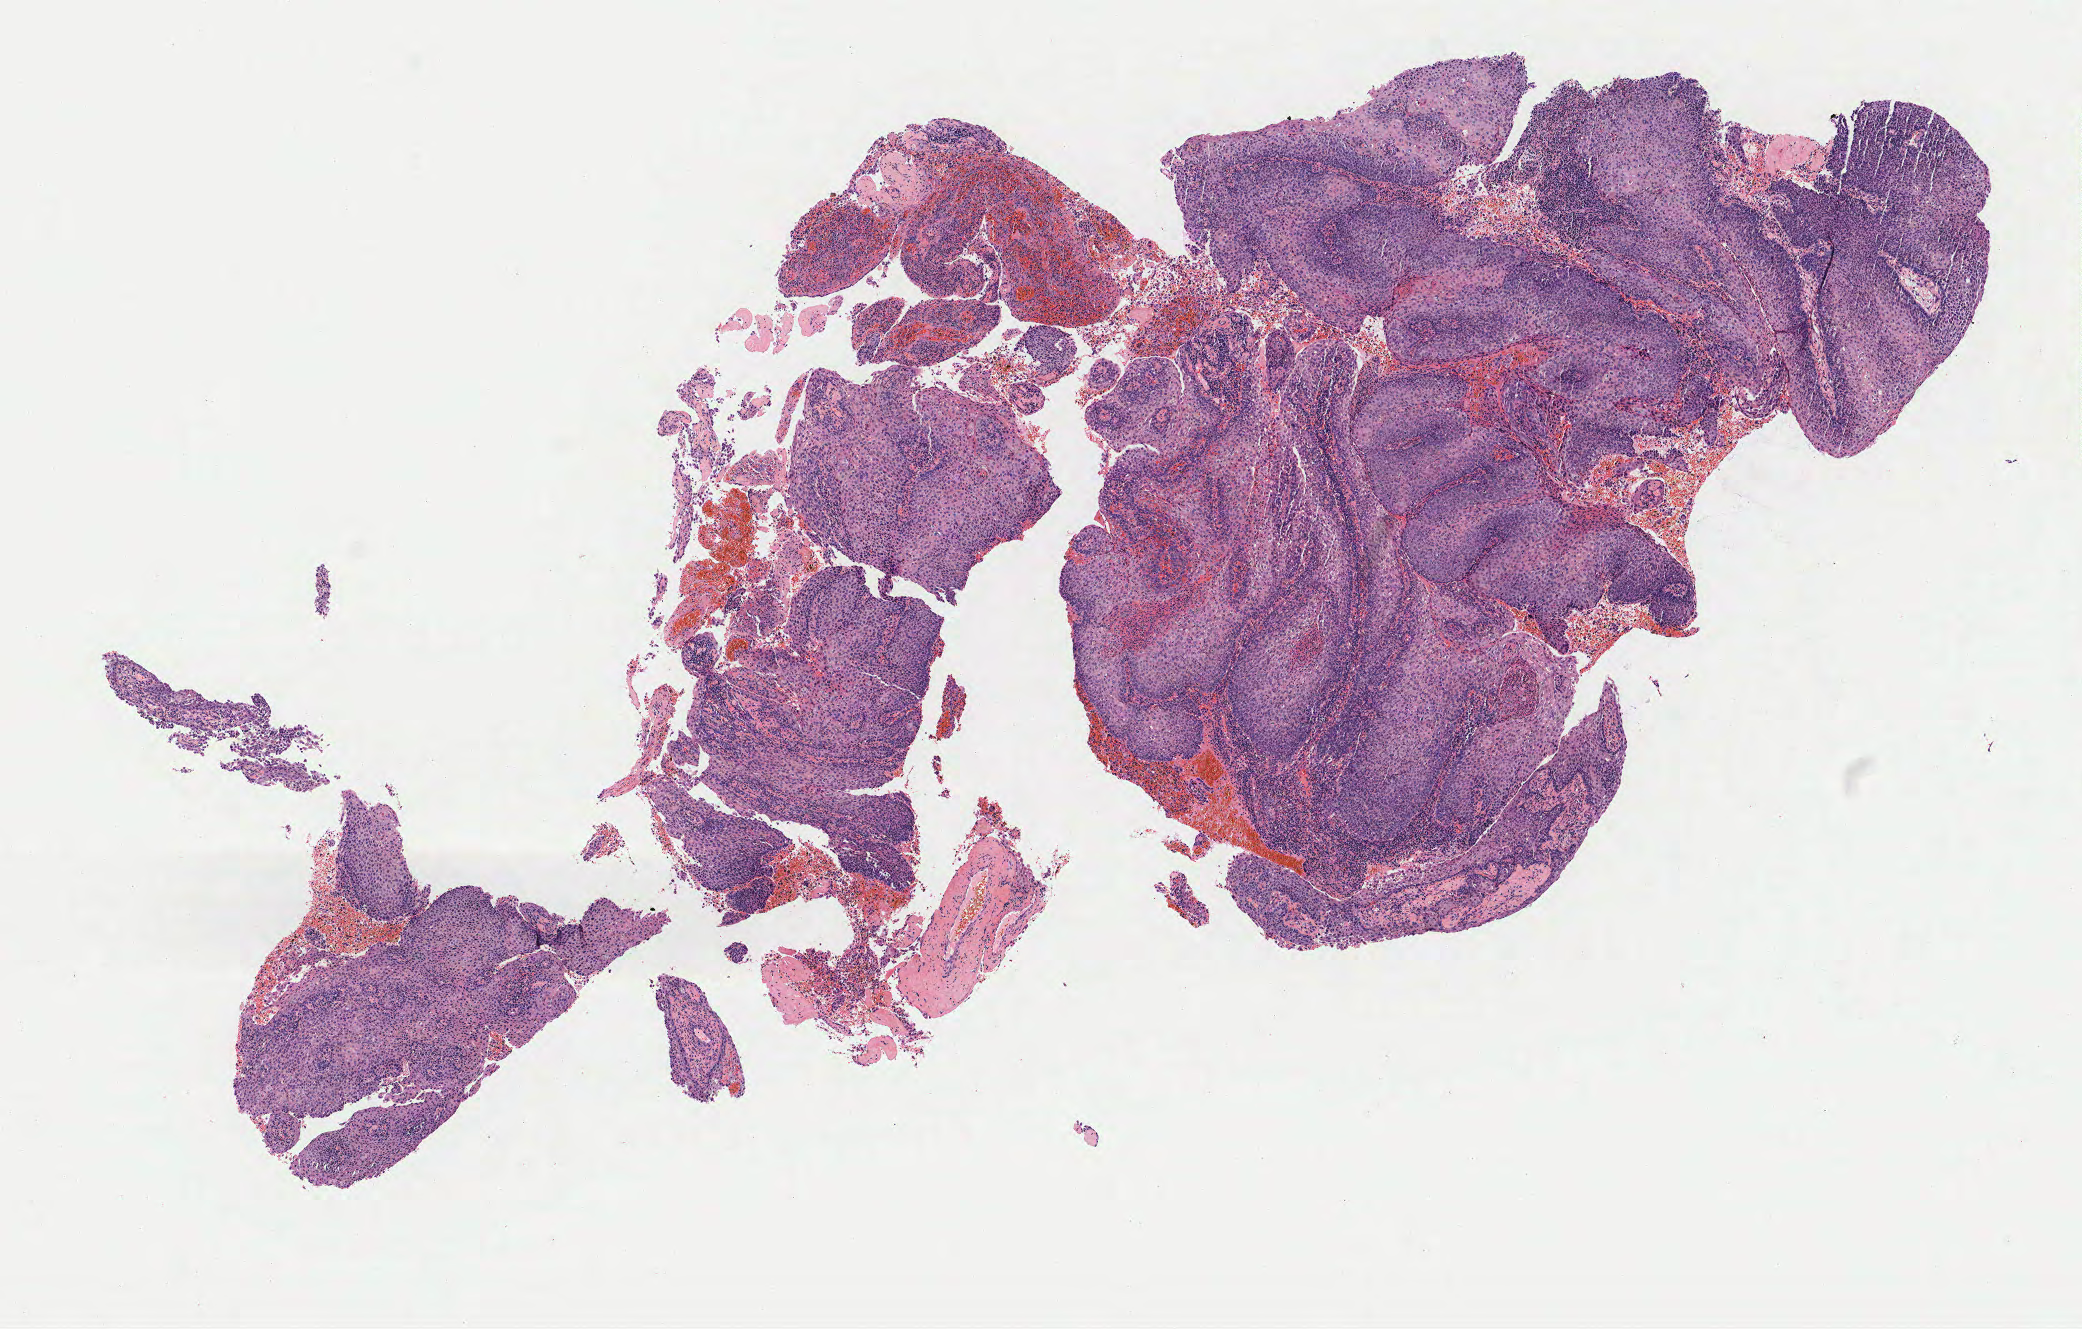
Haematoxylin and eosin whole-slide image, low-resolution overview of the scanned area, about 8.3 x 5.3 mm; specimen: tumor tissue; site: cervix. Female patient, 47 years old.
Diagnosis: Squamous cell carcinoma, keratinizing, NOS.